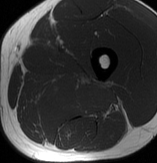
MRI of an extremity soft-tissue mass, one axial slice; position 41 of 70 along the scan axis; MR volume resampled by the dataset authors to the PET/CT grid (not the native acquisition matrix); 157 × 163 image matrix, field of view 153 × 159 mm. Male patient. From the clinical record (not read from this slice): histological type: extraskeletal osteosarcoma; grade: high; site of the primary tumour: left adductur.
Structures marked on this image (expert contour drawn on MRI and transferred to this co-registered scan by the dataset authors):
- gross tumour volume (mass): bounding box (x1, y1, x2, y2) in pixels: (22, 71, 123, 121)